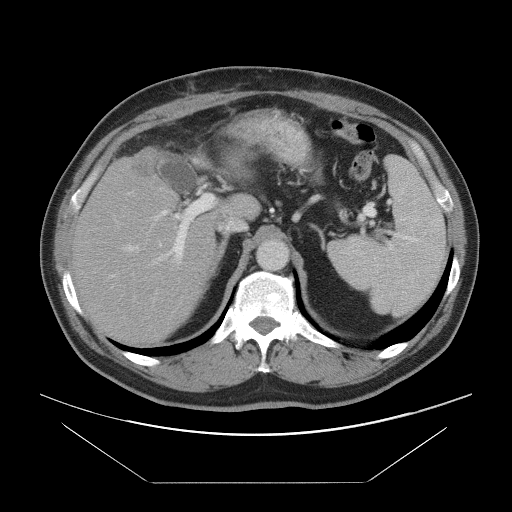
Contrast-enhanced abdominal CT, one axial slice. Position 59 of 97 along the scan axis. 120 kVp. Intravenous contrast given. Soft-tissue window (W 400 / L 40 HU). 512 × 512 image matrix, field of view 442 × 442 mm. Male patient, age 62 years. From the clinical record (not read from this slice): diagnosis: colorectal cancer liver metastases, imaged before liver resection; multiple liver metastases: no; largest metastasis: 7 cm; disease in both lobes: yes.
Outlined on this slice (outlined manually by an expert reader):
- hepatic veins: bounding box <125,187,168,252> (left, top, right, bottom; pixels)
- liver: <75,120,260,343>
- planned liver remnant (the part of the liver to remain after resection): <75,176,227,343>
- portal vein (with intrahepatic branches): <128,192,214,272>
- liver metastasis: <130,154,152,178>